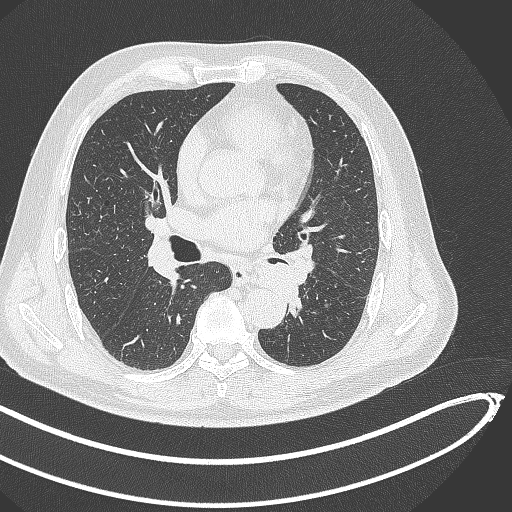
Chest CT, one axial slice. Position 250 of 468 along the scan axis. Reconstruction kernel B70f. 120 kVp. Lung window (W 1500 / L -600 HU). 1 mm slice thickness. 512 × 512 image matrix, field of view 400 × 400 mm. Patient: male, 64 years. Case-level facts recorded for this patient, not image findings: clinical TNM (as recorded): T1c N0 M0.
Outlined on this slice (bounding box drawn by a radiologist):
- lung tumour (recorded histology: squamous cell carcinoma): bounding box [x1, y1, x2, y2] px = [252, 259, 307, 307]